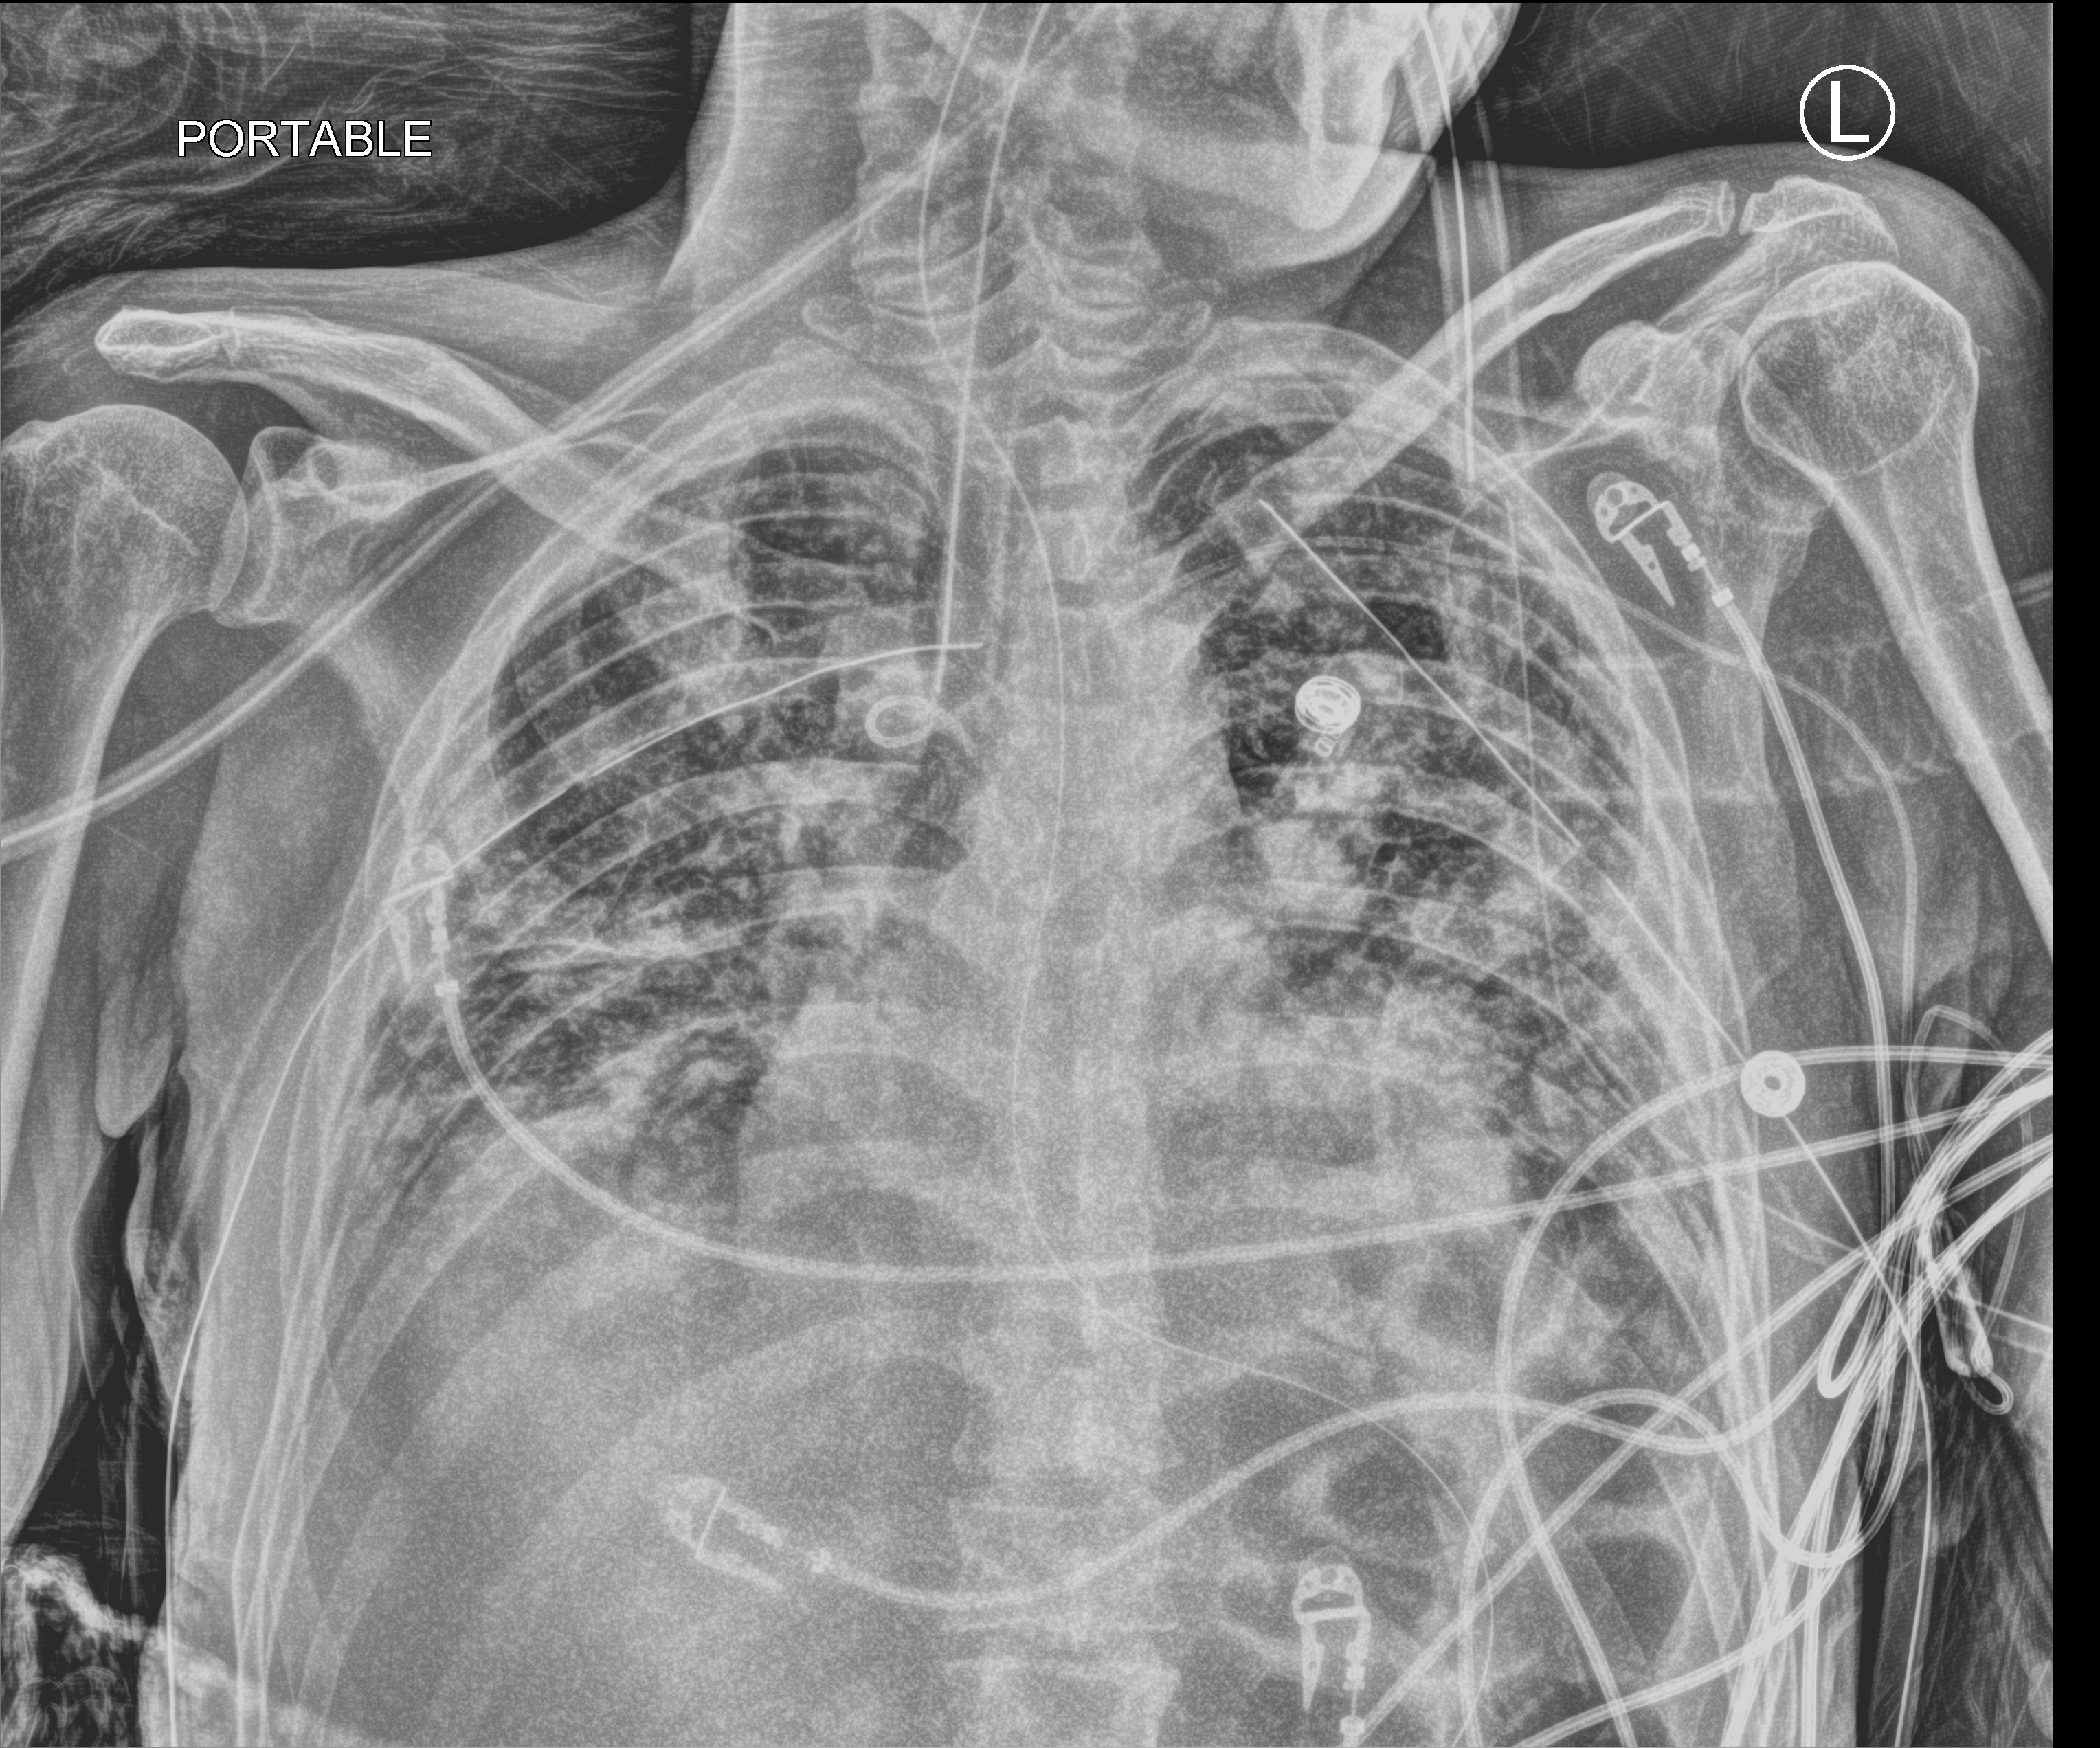
Portable chest radiograph, anteroposterior (AP) projection. Male patient hospitalised with COVID-19, age 18–59 years.
From the hospital-stay record, not from the radiograph (when in the stay this image was taken is not recorded):
- chronic kidney disease (admission record): no
- admitted to intensive care during this hospital stay: yes